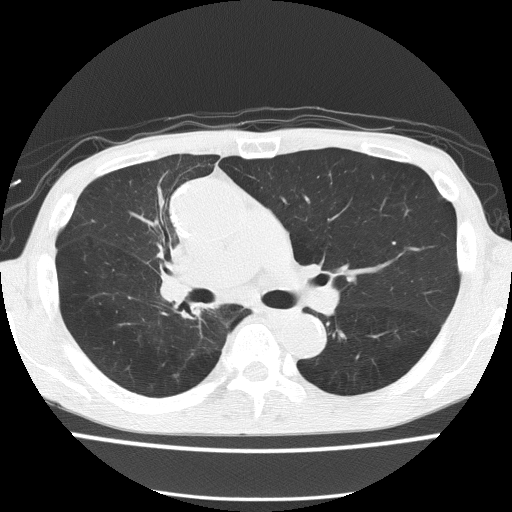
Low-dose screening chest CT, one axial slice. Slice 90 of 150 in the series (ordered by position). Reconstruction kernel FC51. 120 kVp. Lung window (W 1500 / L -600 HU). 2 mm slice thickness. 512 × 512 image matrix.
Structures marked on this image (expert manual segmentation):
- lesion 1 (tumor, hilum of right lung): box from (x=161, y=276) to (x=193, y=300) px